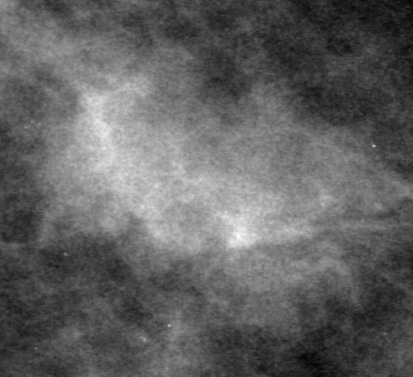
Region of interest cut from a scanned film mammogram (one marked finding), left breast, MLO view.
Mass, shape lobulated, margins obscured; BI-RADS assessment category 0 (incomplete: needs additional imaging); subtlety rating 5 on a 1 (subtle) to 5 (obvious) scale; pathology (as recorded): malignant.